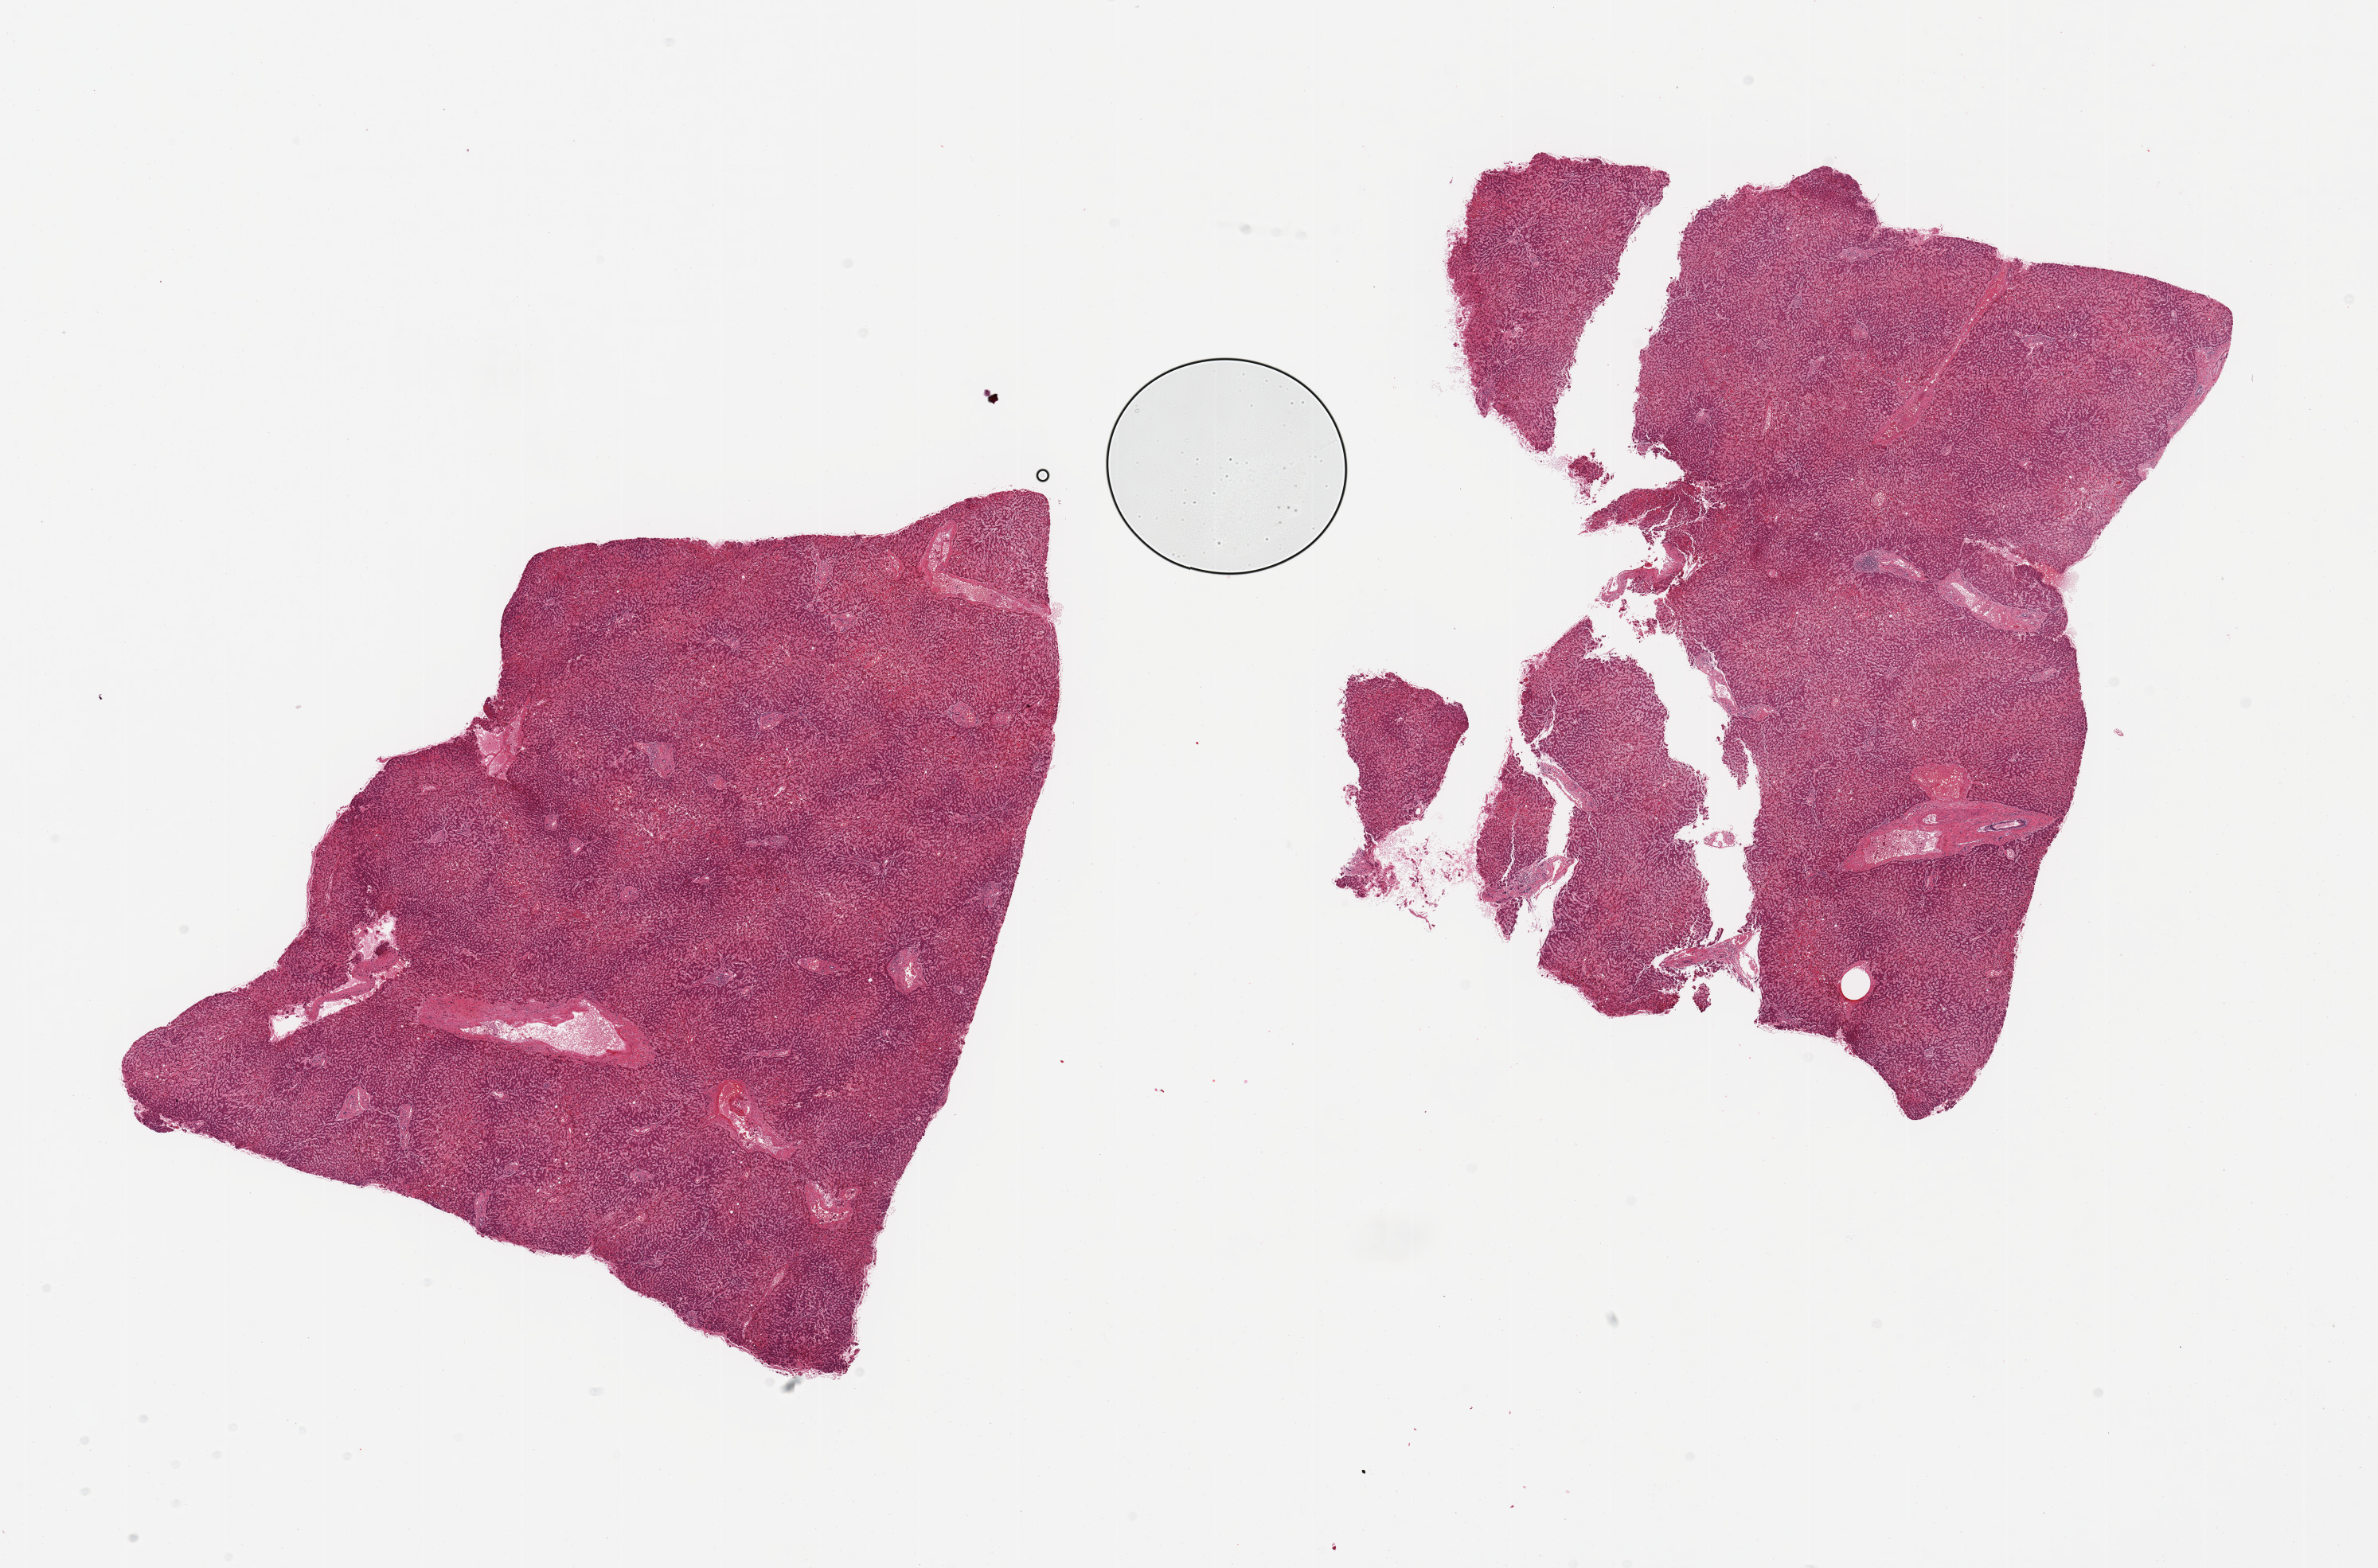
Whole-slide image, hematoxylin and eosin (H&E) stain — whole scanned area (about 23.6 x 15.6 mm) shown as a low-resolution overview. PAXgene-fixed paraffin-embedded (PFPE) section. Sampled site (target tissue): liver. Tissue donor sample. Male donor.
Pathologist's review note for this sample: 2 pieces, moderate congestion.